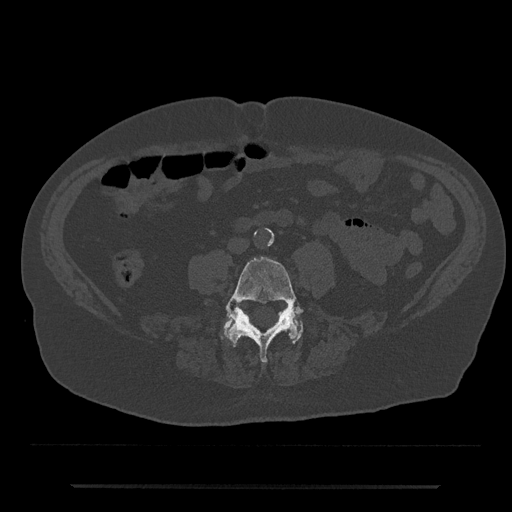
CT including the spine, one axial slice. Position 344 of 797 along the scan axis. Reconstruction kernel Br40s/3. 120 kVp. Bone window (W 1800 / L 400 HU). 0.5 mm slice thickness. 512 × 512 image matrix. Male patient, age 80 years. Case-level facts recorded for this patient, not image findings: primary cancer: prostate; vertebrae with lytic lesions (as recorded): L1, T11.
Annotated regions visible in this slice (semi-automatic segmentation, software-assisted and operator-edited):
- L4 vertebra: bounding box (x1, y1, x2, y2) in pixels: (226, 256, 313, 363)
- L5 vertebra: (222, 316, 303, 343)